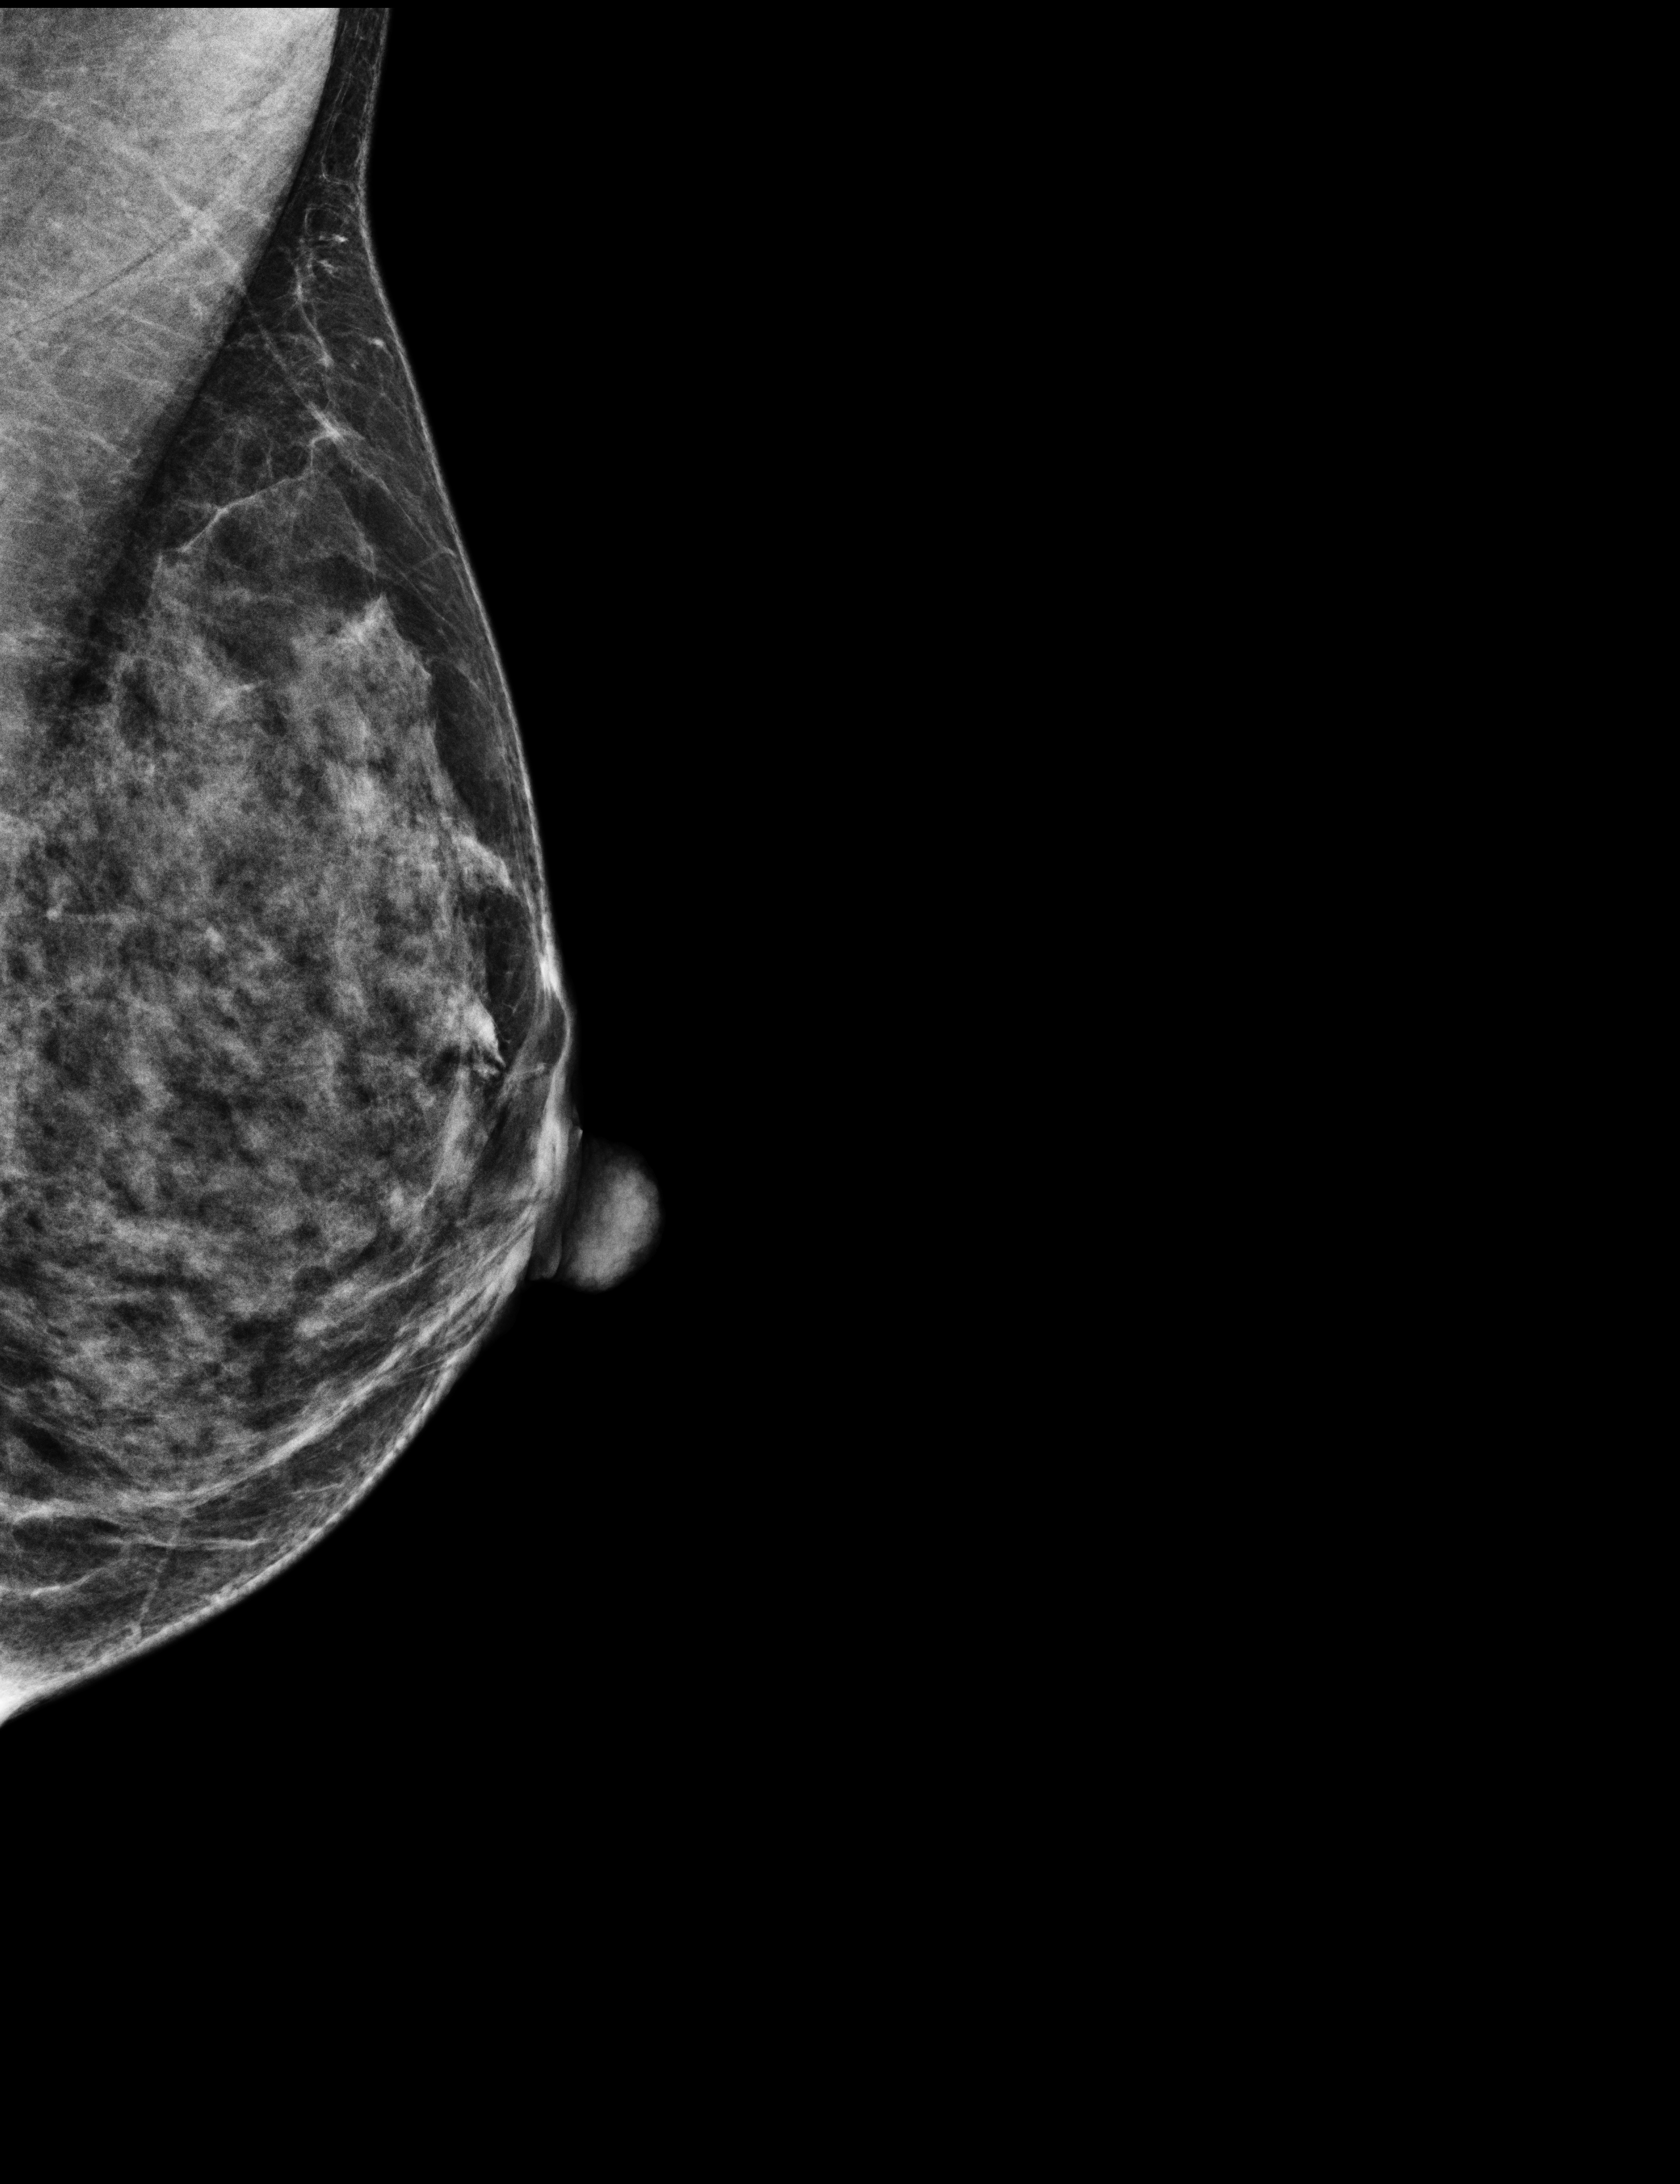
Annual screening mammography examination, compressed breast thickness 35 mm, system: Selenia Dimensions. Female patient, age 43 years.
Image type: full-field digital mammogram. Breast: left. Projection: MLO view.